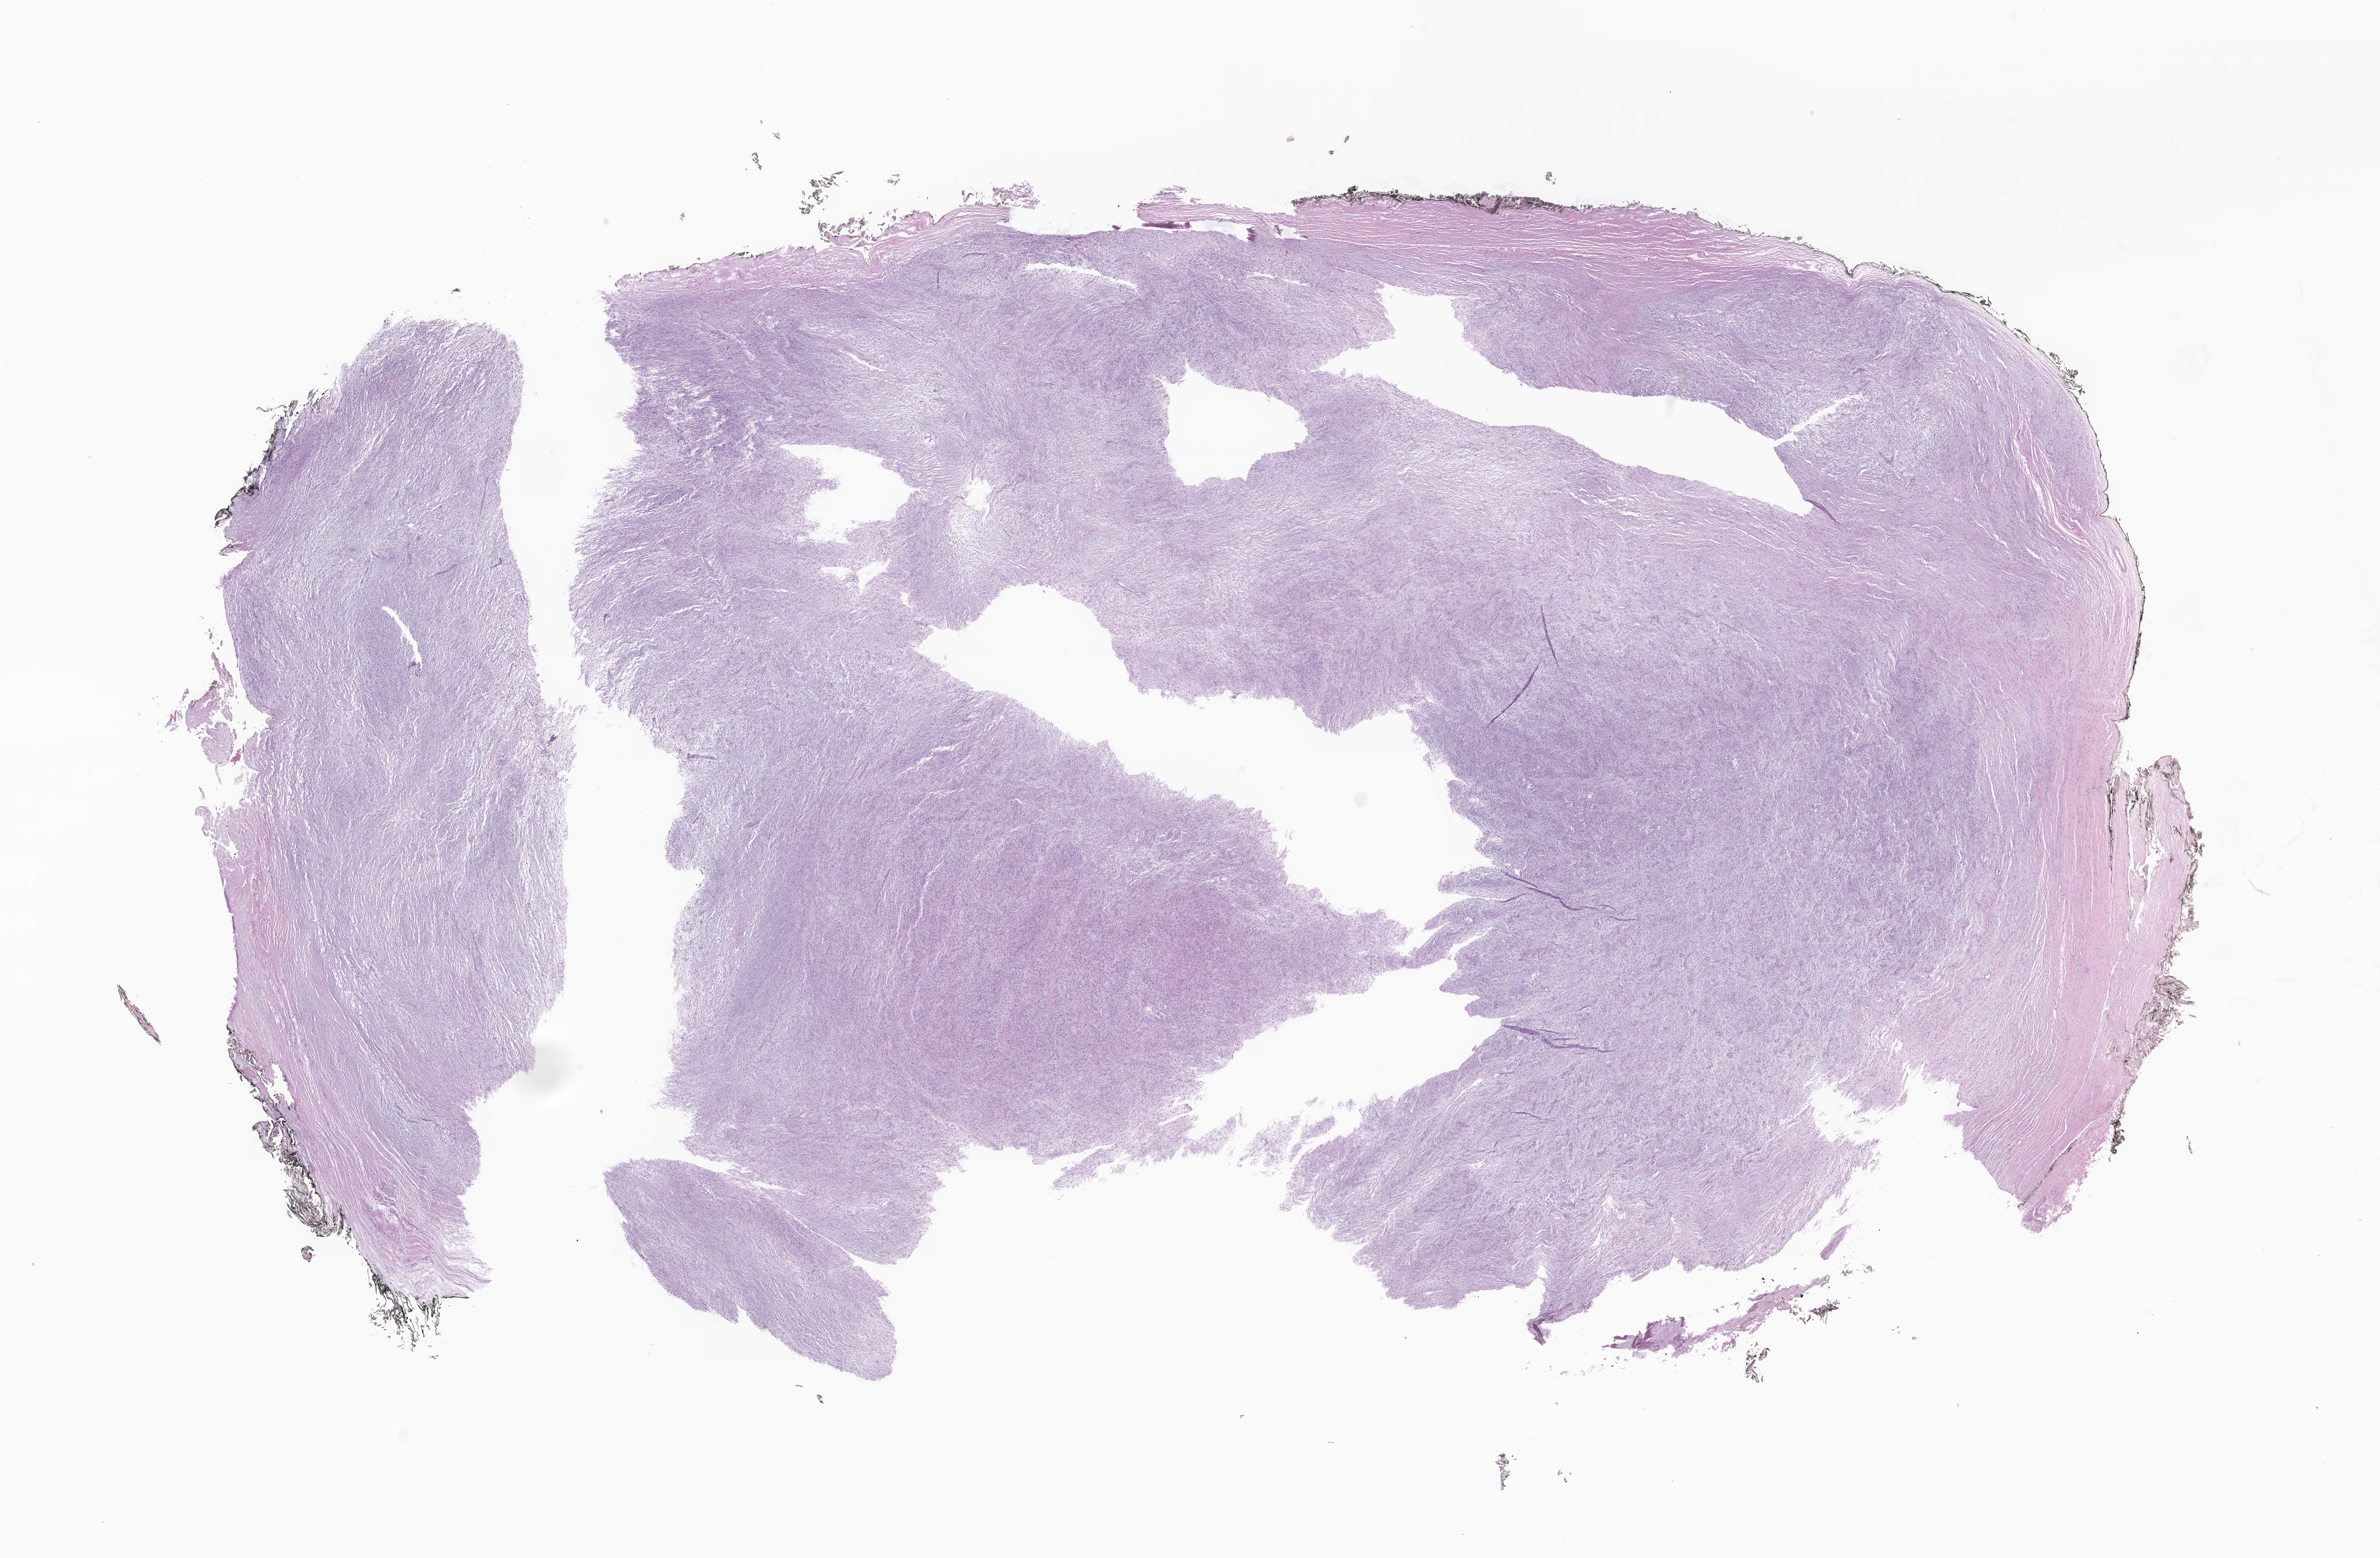
Whole-slide image, hematoxylin and eosin (H&E) stain of tumor tissue from the scrotum — whole scanned area (about 25.3 x 16.6 mm) shown as a low-resolution overview. Formalin-fixed paraffin-embedded section. Patient male; age 187 months (15 years 7 months).
Recorded diagnosis: Myxofibrosarcoma.